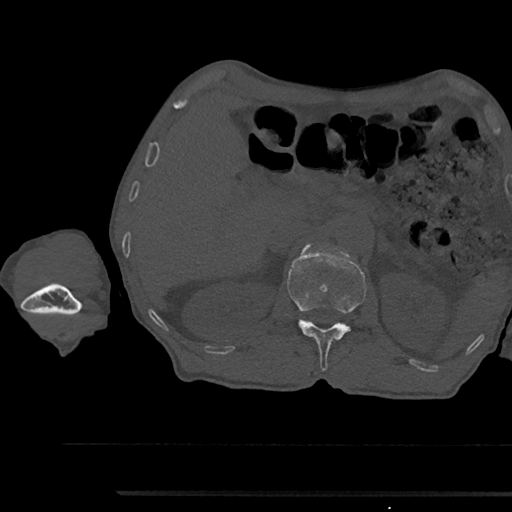
CT including the spine, one axial slice; slice 632 of 797 in the series (ordered by position); reconstruction kernel Br40s/3; 120 kVp; bone window (W 1800 / L 400 HU); 512 × 512 image matrix, field of view 367 × 367 mm. Patient: male, 79 years. From the clinical record (not read from this slice): primary cancer: prostate.
Outlined on this slice (semi-automatic segmentation, software-assisted and operator-edited):
- L1 vertebra: bounding box [x1, y1, x2, y2] px = [287, 244, 366, 370]